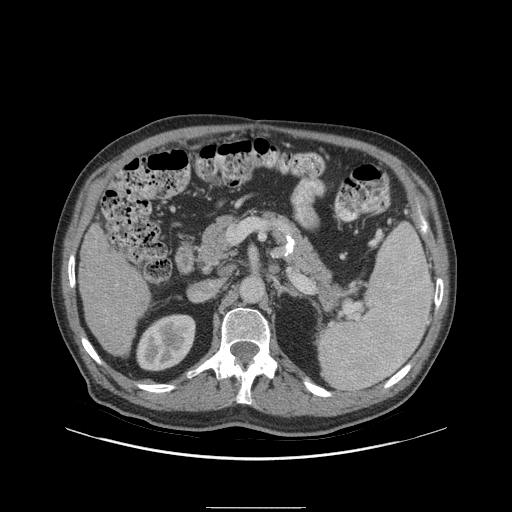
Contrast-enhanced abdominal CT (liver protocol), one axial slice; position 41 of 105 along the scan axis; reconstruction kernel STANDARD; 140 kVp; soft-tissue window (W 400 / L 40 HU); 512 × 512 image matrix, field of view 440 × 440 mm. Case-level facts recorded for this patient, not image findings: diagnosis: hepatocellular carcinoma (patient treated with transarterial chemoembolisation; whether this scan precedes or follows treatment is not stated here); TNM stage (as recorded): Stage-I; Child-Pugh class: A; tumour nodularity: uninodular; tumour size: 5.1 cm.
Structures marked on this image (semi-automatic segmentation, software-assisted and operator-edited):
- liver parenchyma outside the tumour (the mass and vessels are separate outlines, so this box may not span the whole liver): bounding box (x1, y1, x2, y2) in pixels: (78, 224, 150, 356)